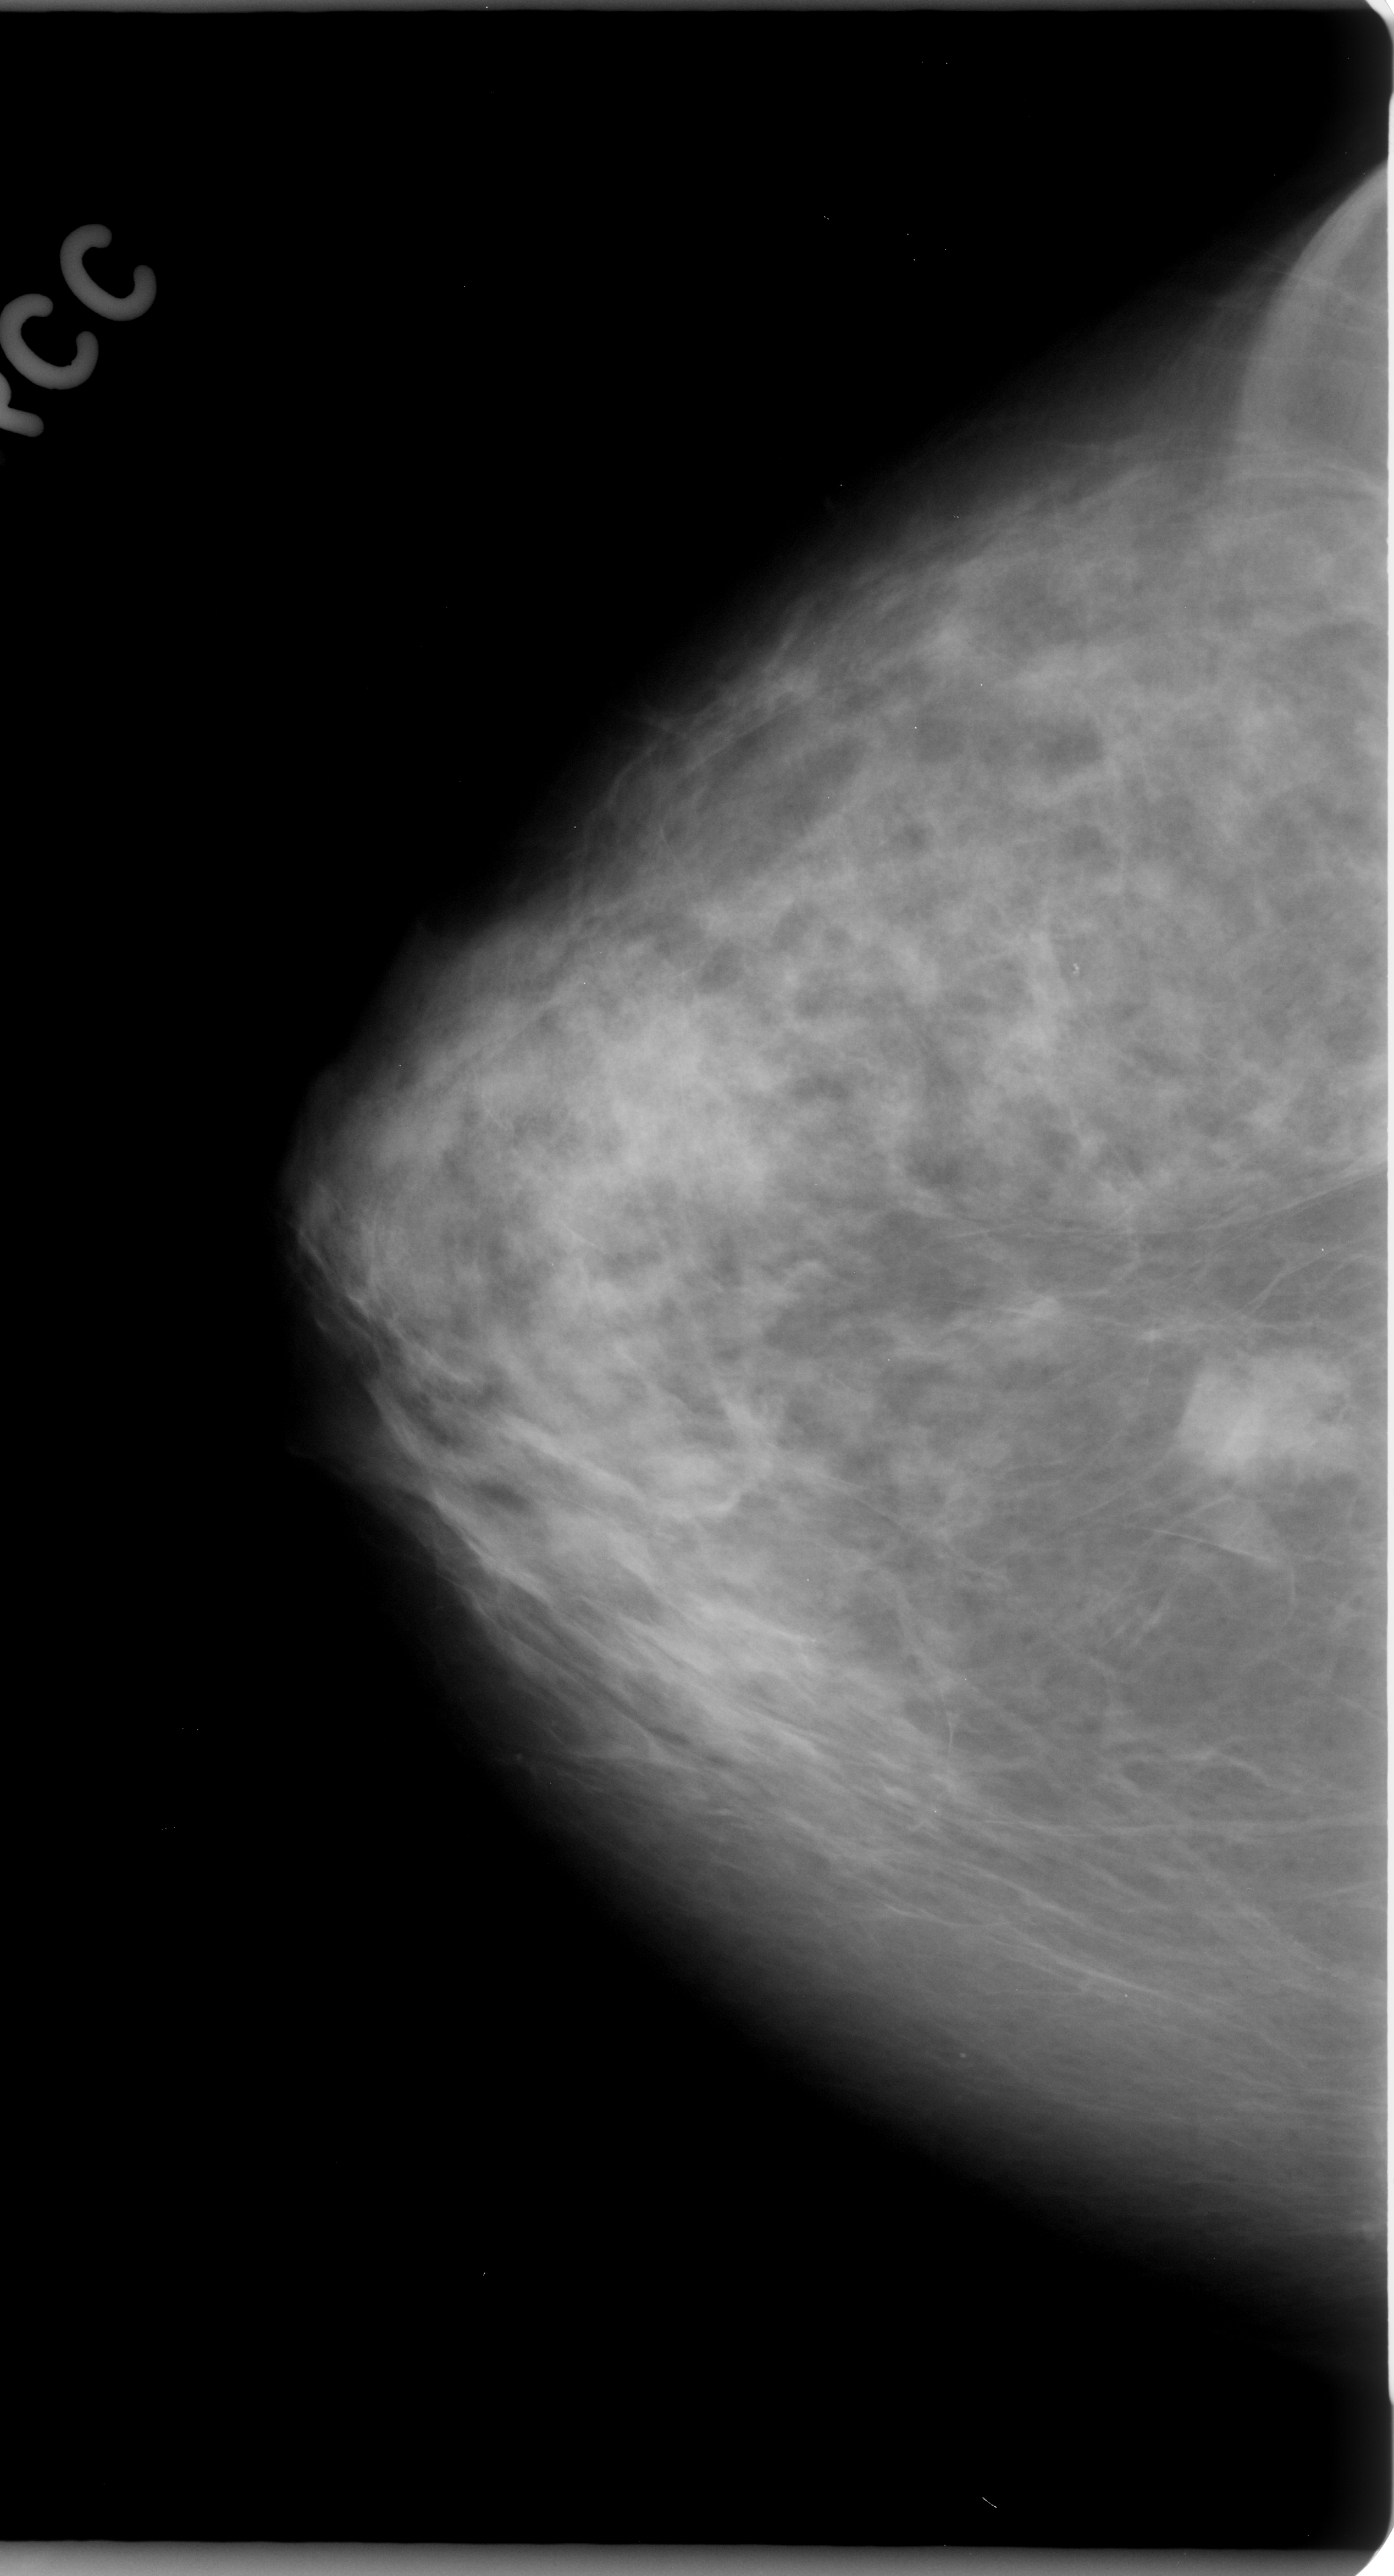
Digitized screen-film mammogram. Right breast. CC view. BI-RADS breast density category 2 (scale 1–4). 1394 × 2576 image matrix.
Expert-marked regions of interest on this image (one box per marked abnormality):
- mass, shape irregular, margins spiculated; BI-RADS assessment category 5; subtlety rating 5 on a 1 (subtle) to 5 (obvious) scale; pathology result (as recorded, not read from the image): malignant: bounding box <1166,1335,1347,1491> (left, top, right, bottom; pixels)